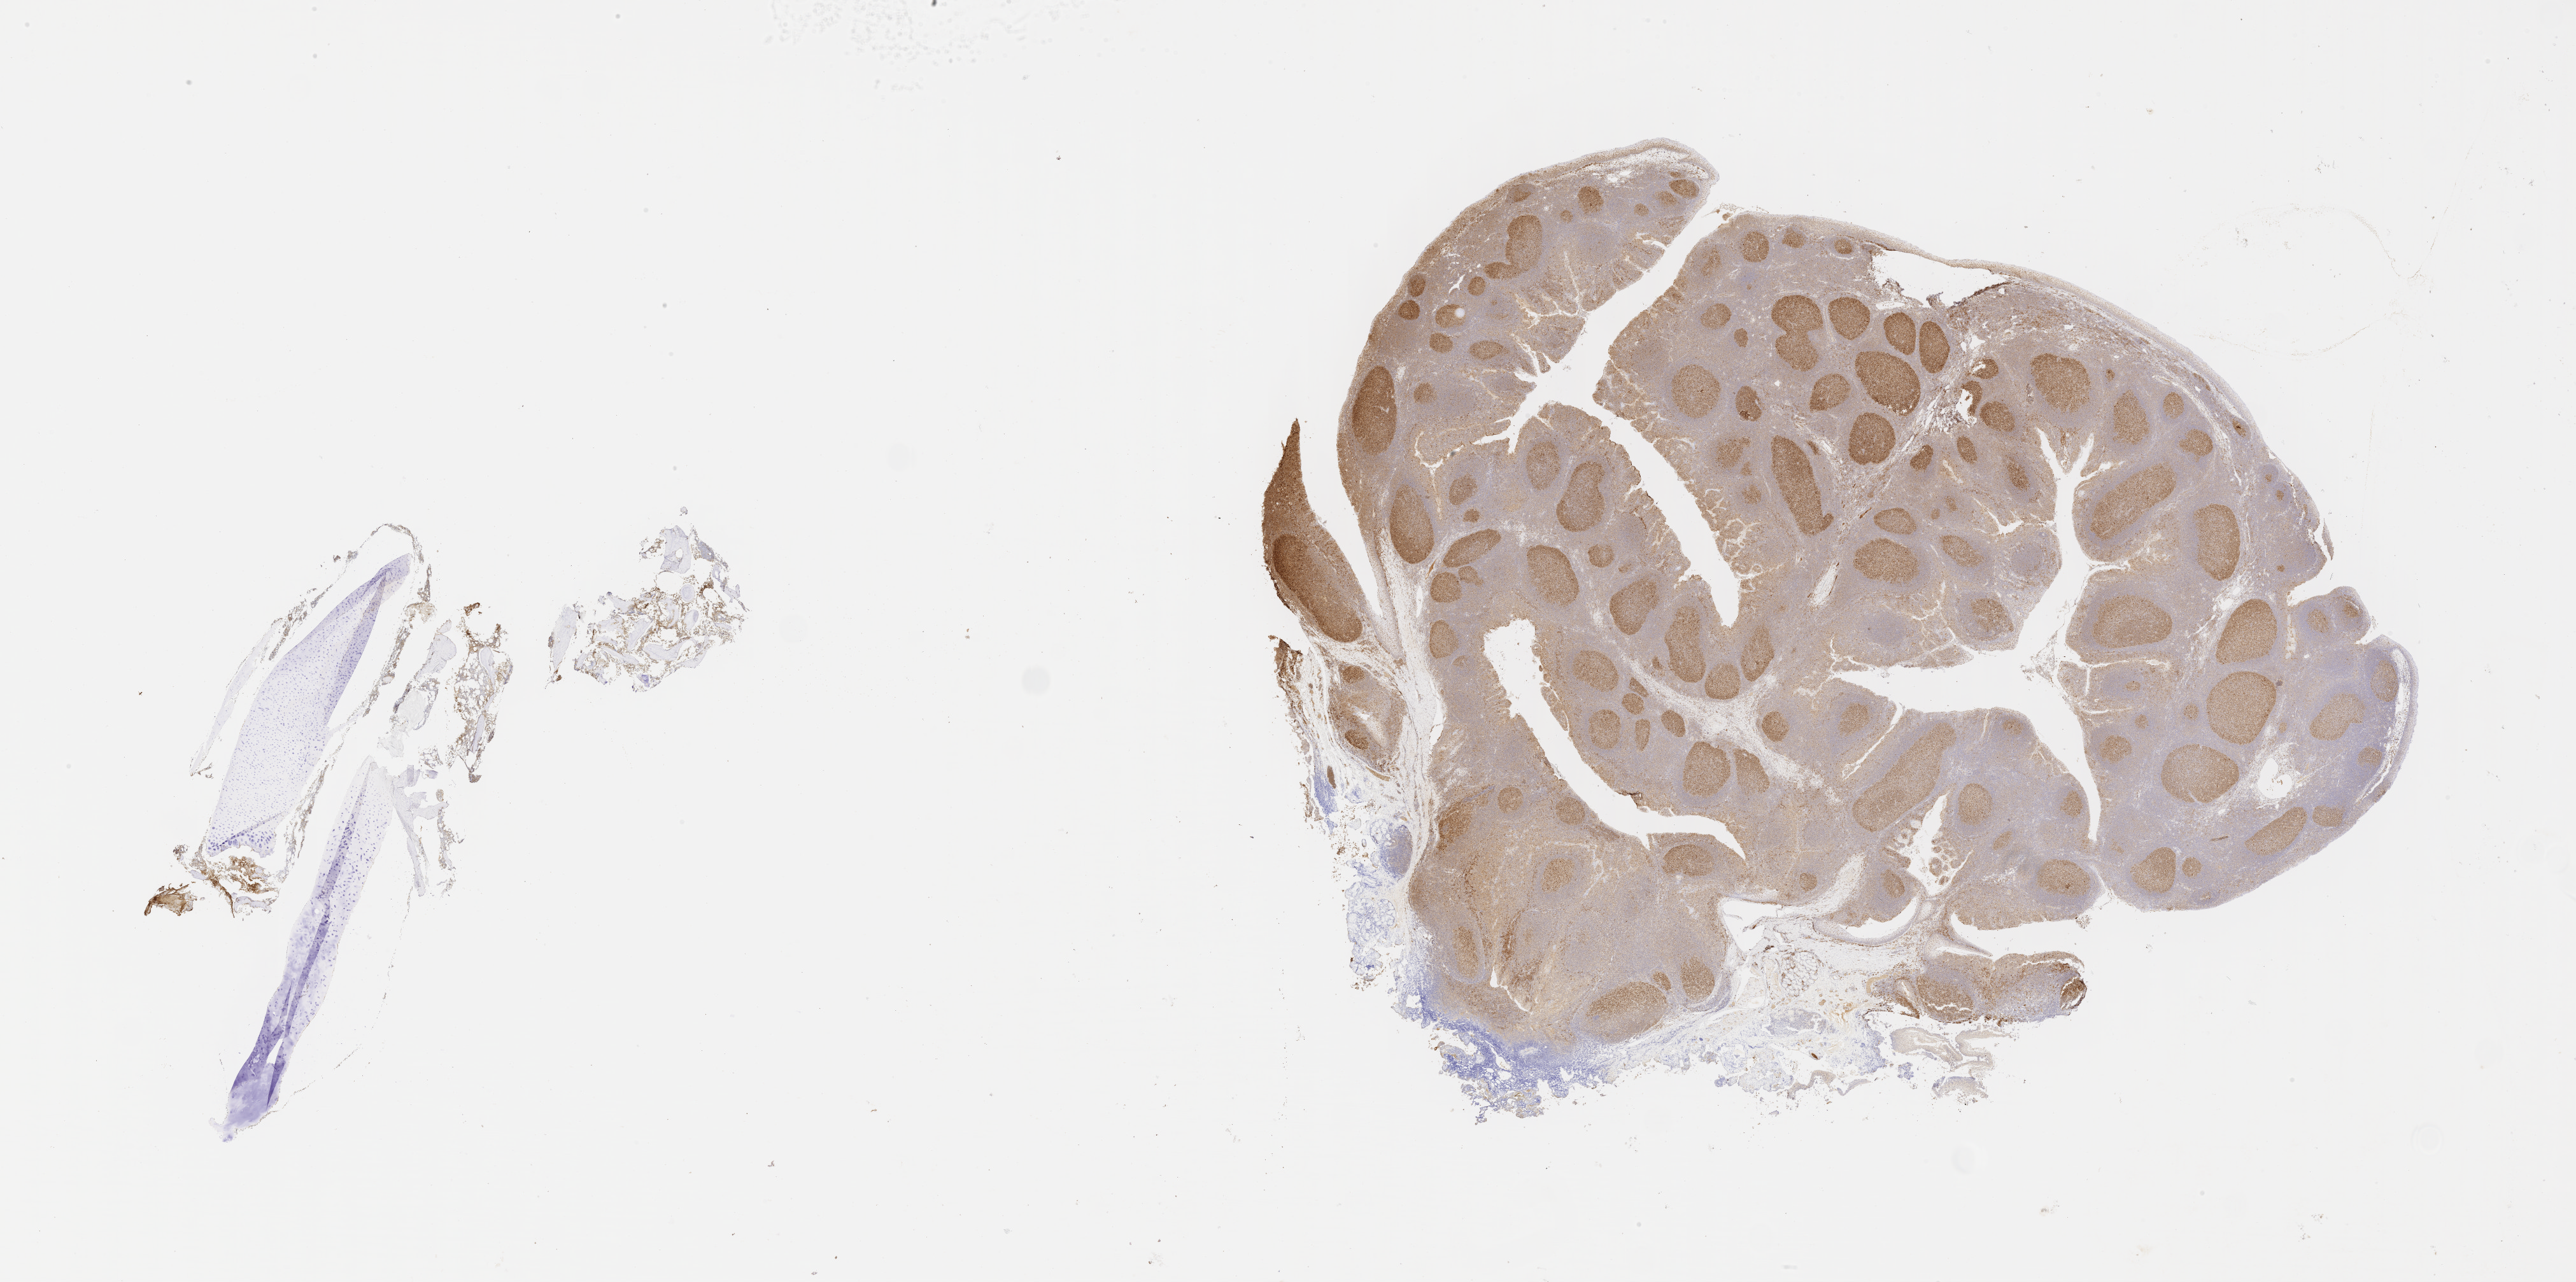
IHC for BCL6, whole-slide image — a low-resolution overview of the entire scanned area, about 32.7 x 16.3 mm; tumor tissue; anatomic site: bone marrow. Female patient, age 11 years.
Diagnosis: Burkitt lymphoma, NOS.